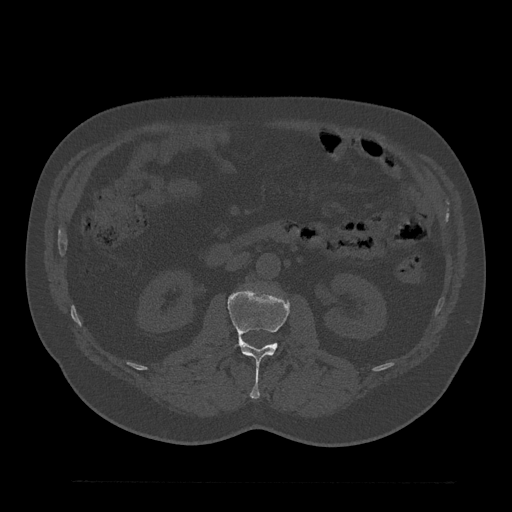
CT including the spine, one axial slice; position 93 of 797 along the scan axis; reconstruction kernel Br40s/3; bone window (W 1800 / L 400 HU); 0.5 mm slice thickness; 512 × 512 image matrix, field of view 430 × 430 mm. Patient: male, 61 years. From the clinical record (not read from this slice): primary cancer: prostate.
Outlined on this slice (semi-automatic segmentation, software-assisted and operator-edited):
- L2 vertebra: bounding box <207,287,289,399> (left, top, right, bottom; pixels)